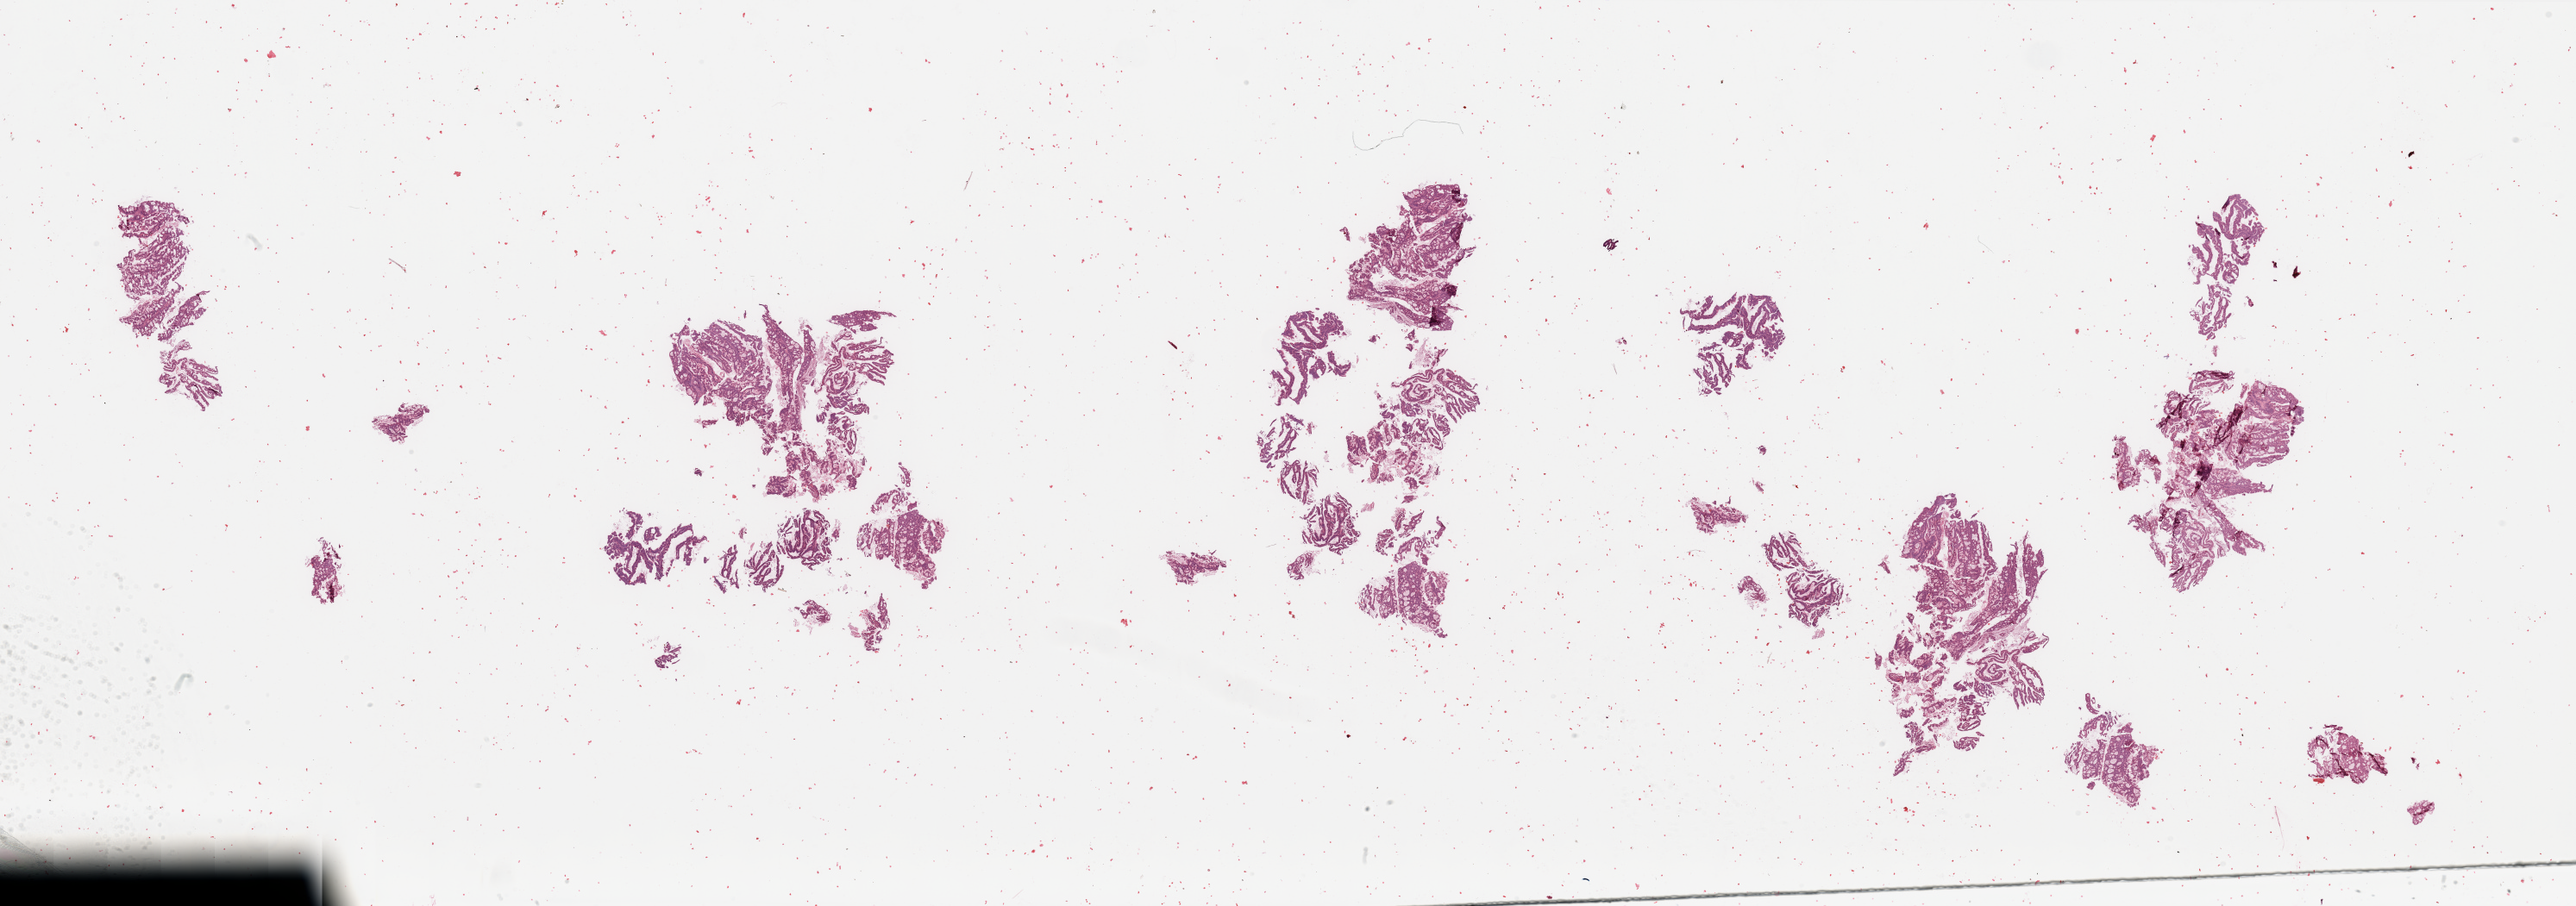
H&E whole-slide image, a low-resolution overview of the entire scanned area, about 47.3 x 16.6 mm (slide scanned at 20x). Tumour tissue sample, sampled site: uterus. Female, 66 y/o. Histologic grade: G1 (well differentiated). Slide review estimates, as recorded: tumour nuclei 90%, necrosis 2%.
Diagnosis: Endometrioid adenocarcinoma, NOS. AJCC pathologic stage: I.